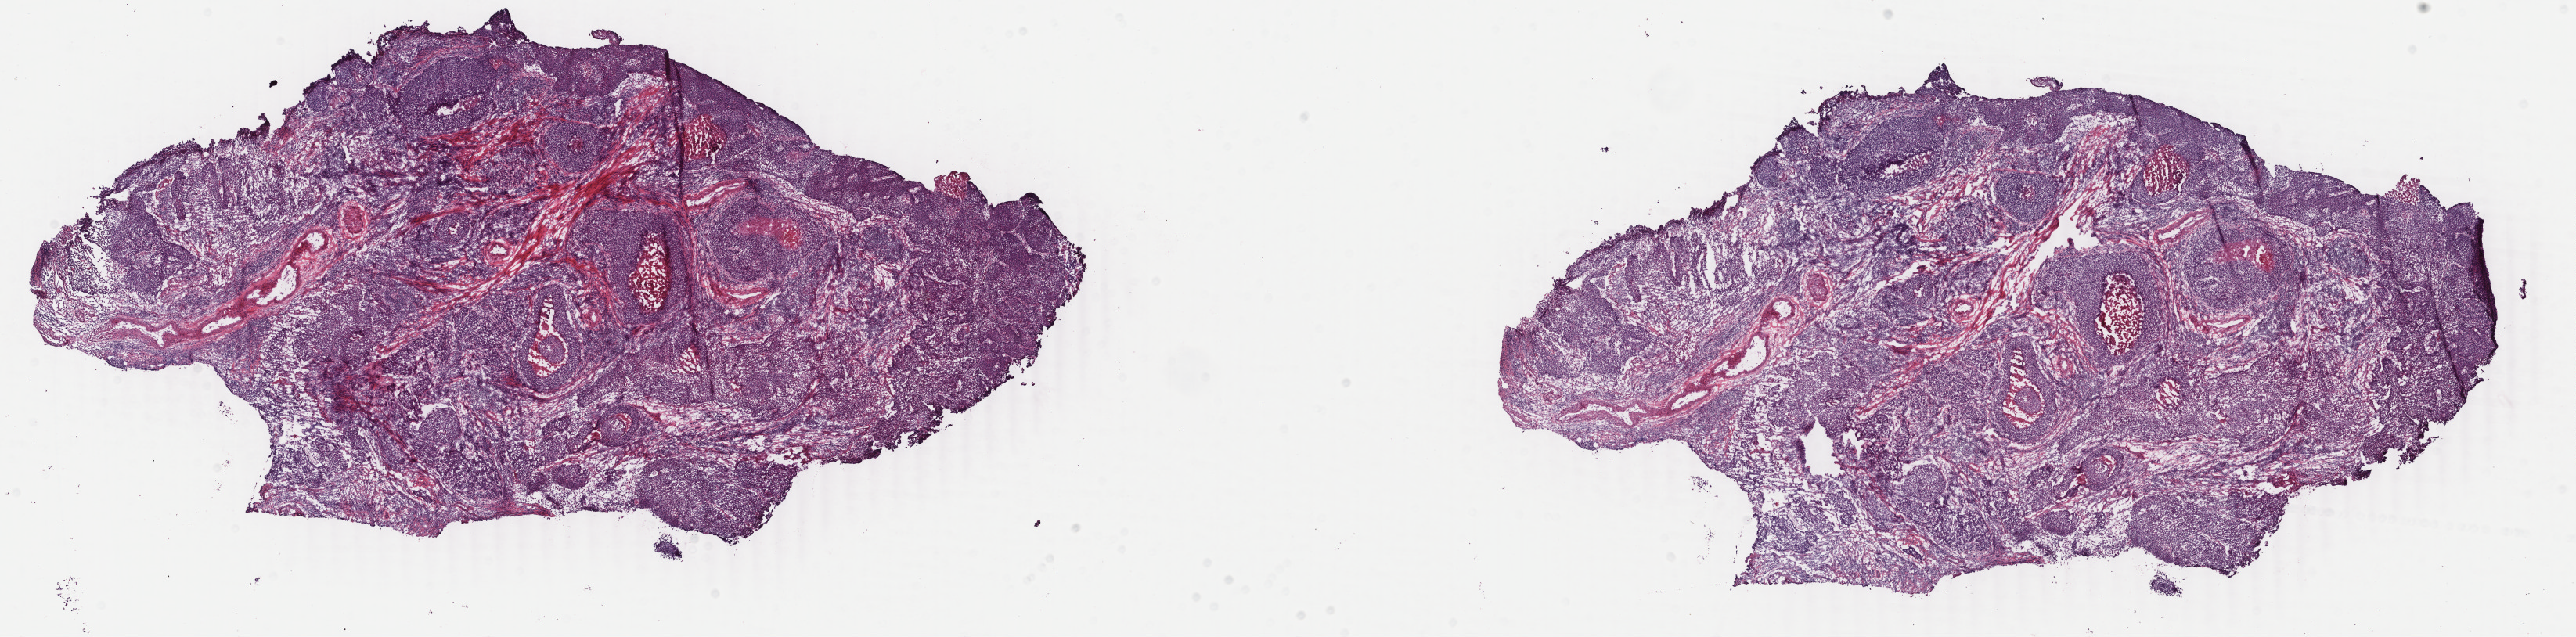
H&E whole-slide image — shown as a low-resolution overview of the whole scanned area (about 26.2 x 6.5 mm, from a 40x scan). Frozen section. Sample: primary tumour, cervix. Female patient; age at initial diagnosis 53 years. Histologic grade: G3 (poorly differentiated). Composition of this section per pathologist review: tumour cells 70%, tumour nuclei 70%, normal cells 0%, stromal cells 25%, necrosis 5%. Inflammatory infiltration, as recorded: lymphocyte infiltration 40%, monocyte infiltration 5%, neutrophil infiltration 50%.
Pathologic diagnosis: Squamous cell carcinoma, NOS (cervix uteri).